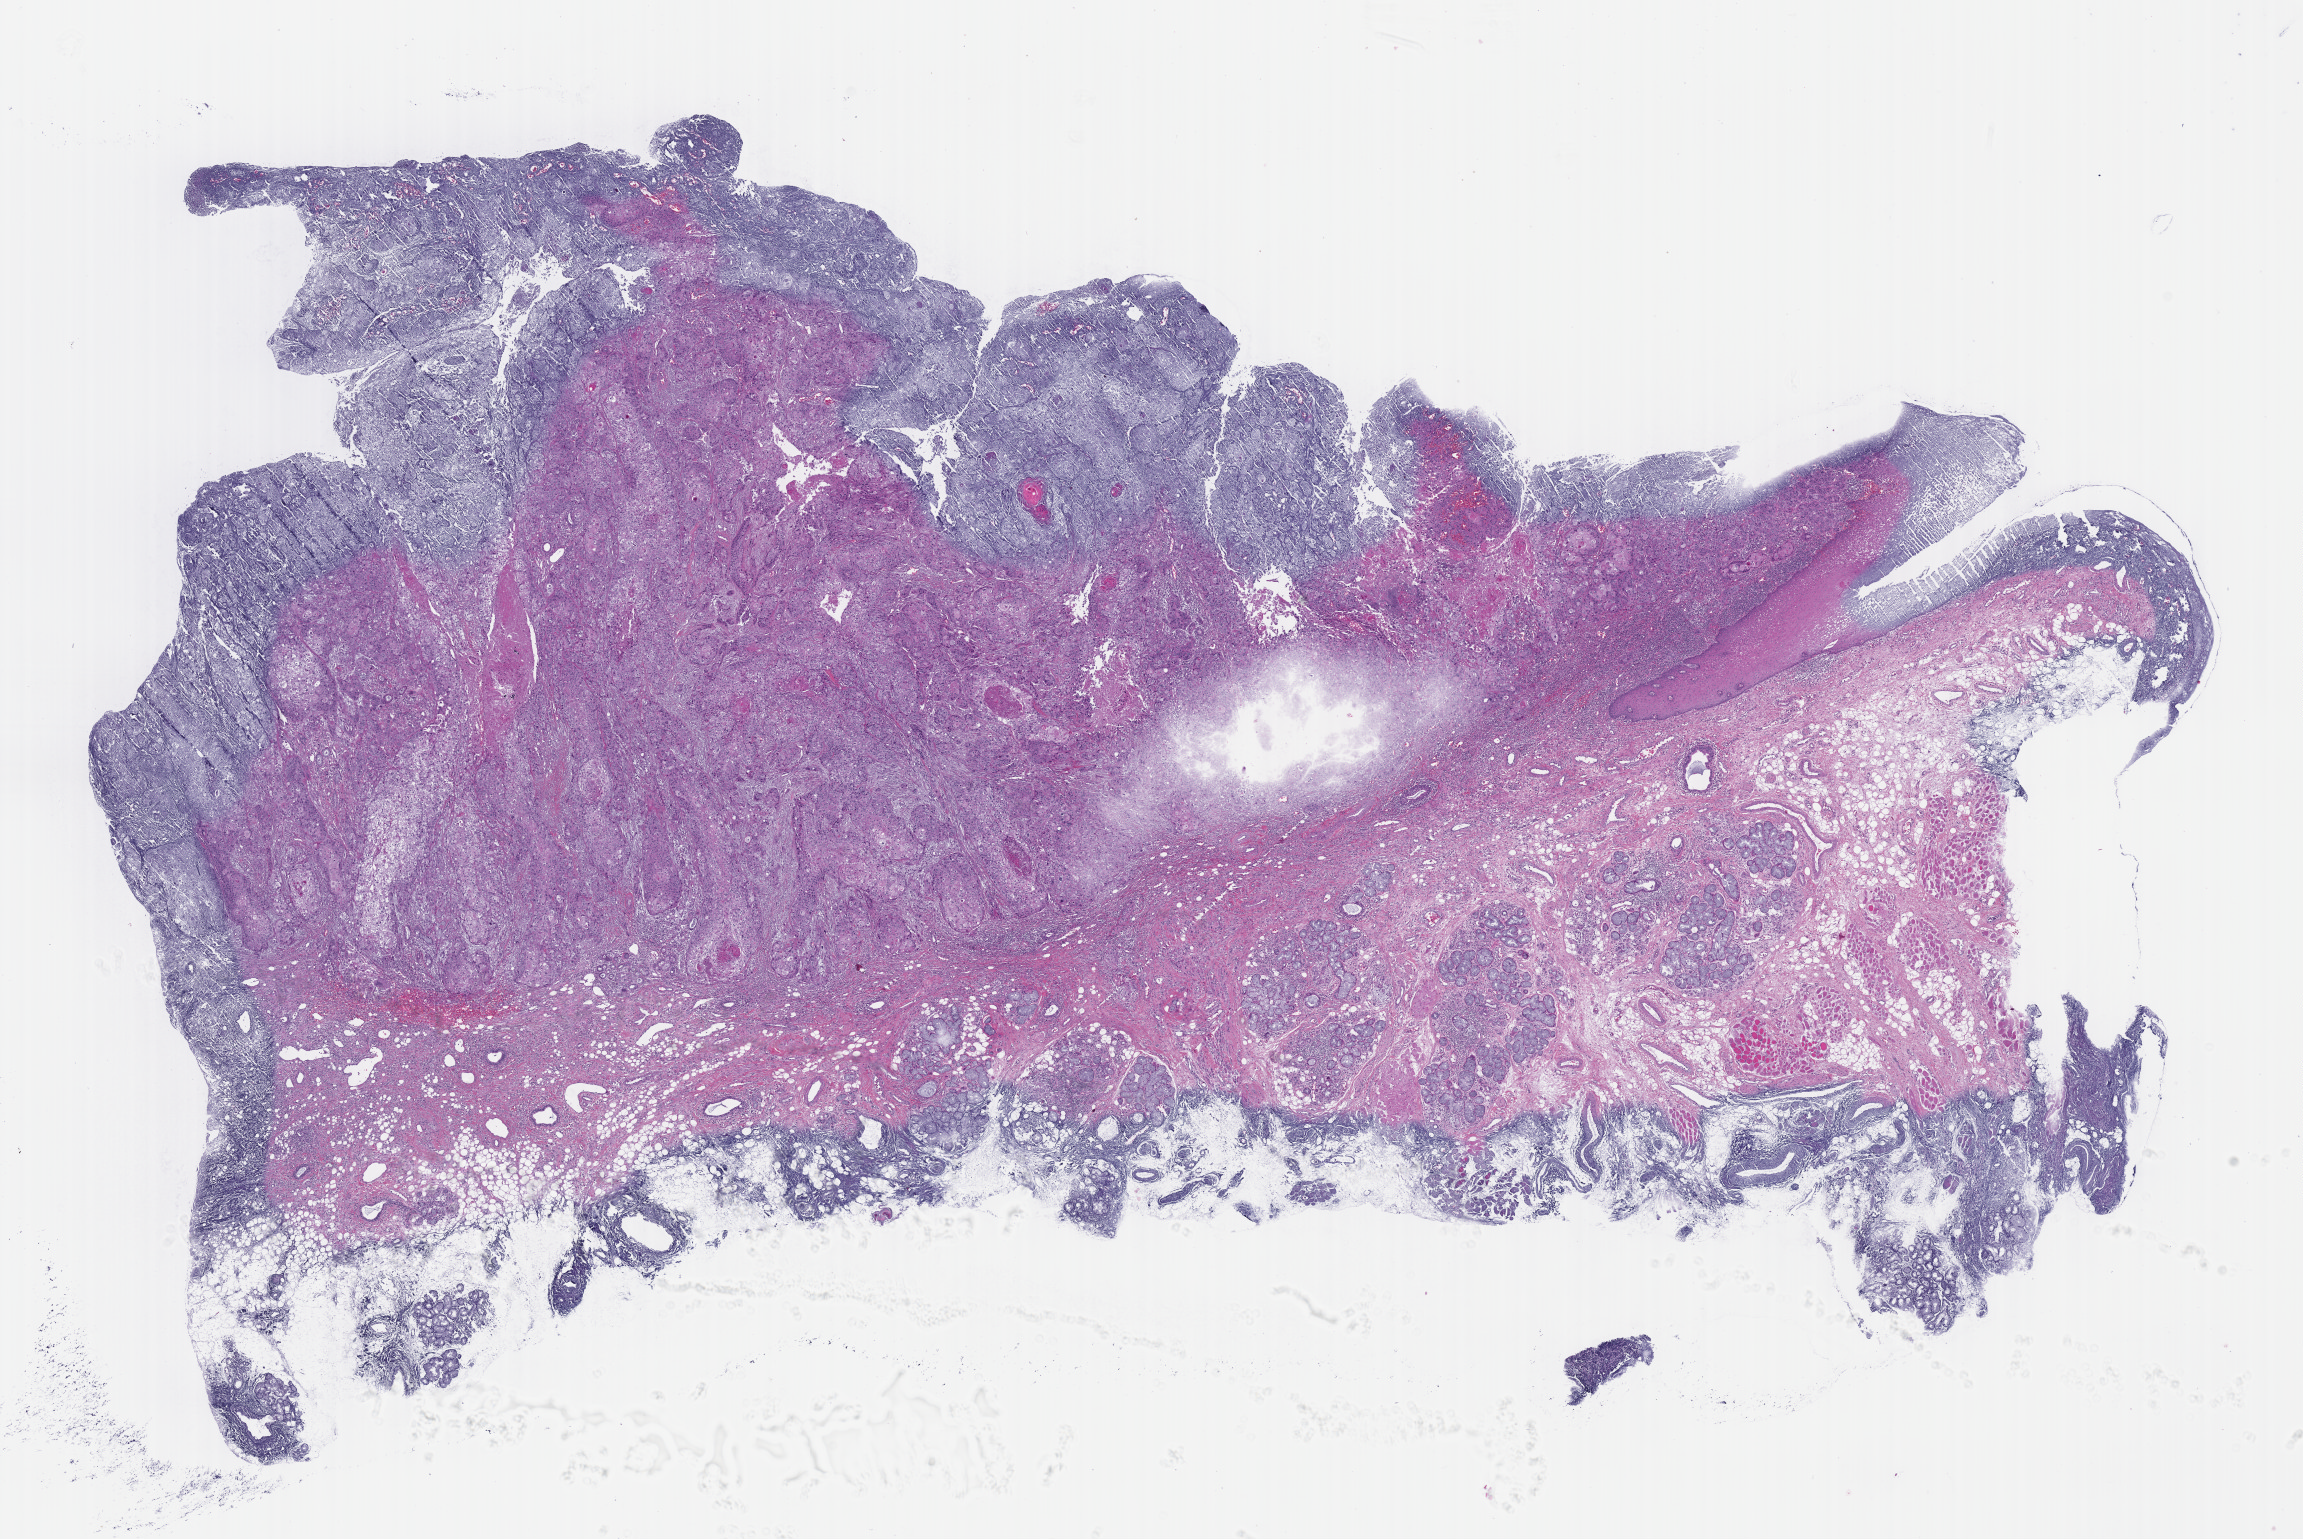
Digitized Hematoxylin and eosin (H&E) stained tissue section (whole slide), low-resolution overview of the scanned area, about 18.6 x 12.4 mm (from a 40x scan). FFPE section. Sample: primary tumour, head and neck. Female patient; age at initial diagnosis 29 years. Histologic grade: GX (grade cannot be assessed).
Diagnosis: Squamous cell carcinoma, NOS (overlapping lesion of lip, oral cavity and pharynx). AJCC pathologic stage: IVA (7th edition).